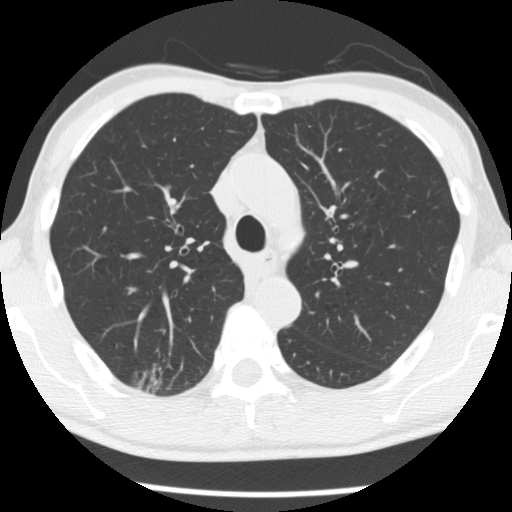
Low-dose screening chest CT, axial slice; baseline screening round; lung window (W 1500 / L -600 HU); standard (soft-tissue) reconstruction kernel (STANDARD); 120 kVp; slice 85 of 277 in the series. Male, age 66 years at enrolment. Former smoker at enrolment.
Expert reader's lesion annotation, bounding box [x1, y1, x2, y2] px = [131, 356, 190, 402]. The screening reader recorded 4 non-calcified nodules or masses ≥4 mm on this exam (right upper lobe, right upper lobe, right upper lobe, left lower lobe); which of them this box marks is not recorded. Participant outcome: lung cancer diagnosed 503 days after this screen — adenocarcinoma, NOS, right upper lobe, undifferentiated (G4), stage IA (AJCC 6th edition), 20 mm at pathology.